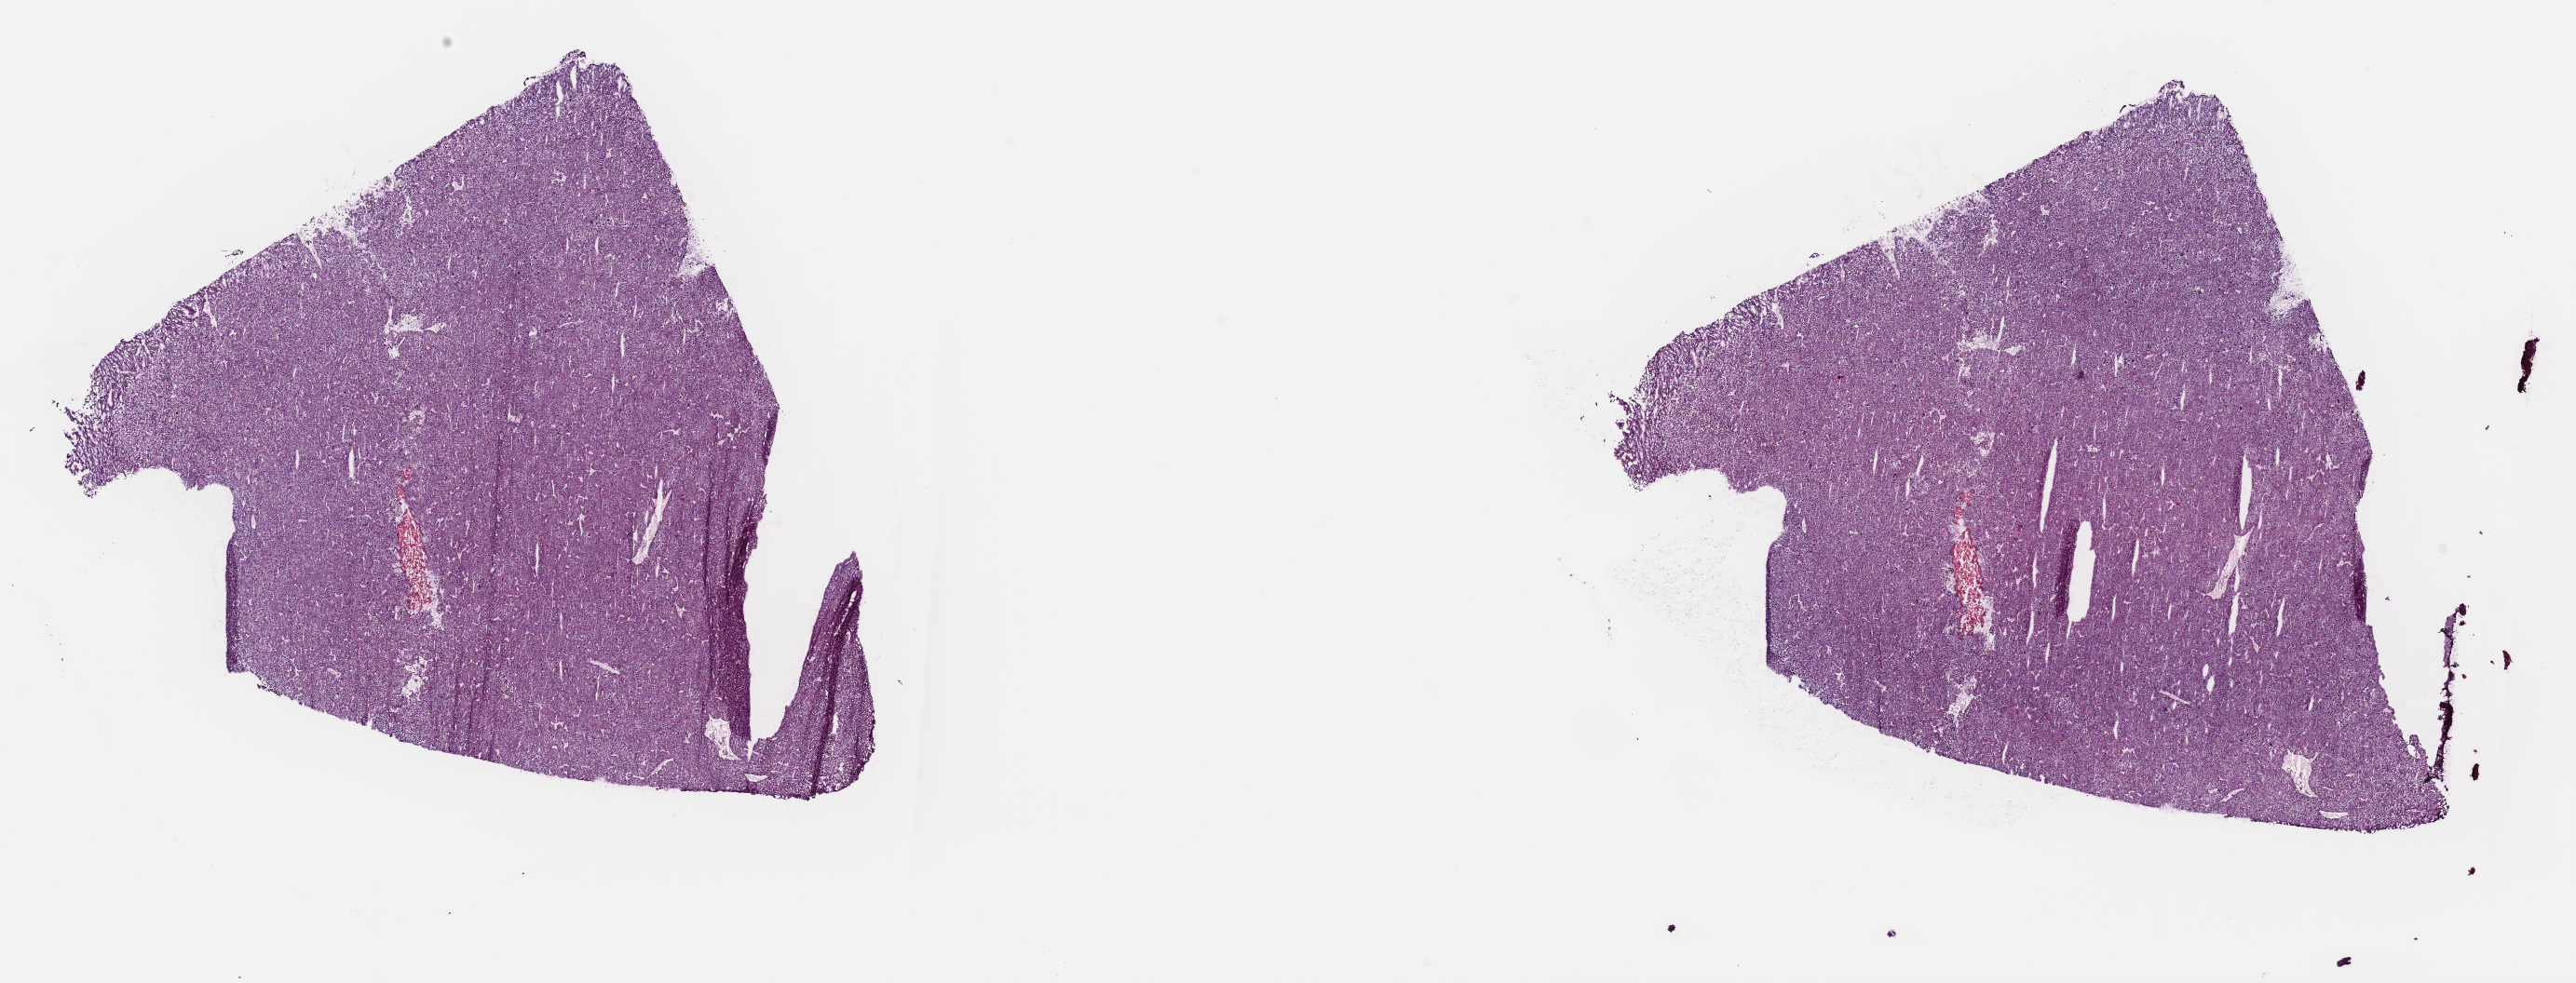
Digitized Hematoxylin and eosin (H&E) stained tissue section (whole slide), whole scanned area (about 21.9 x 8.3 mm, slide scanned at 40x) shown as a low-resolution overview, frozen section from the top of the tissue portion, primary tumour sample from the liver. Female, age 72 years at initial diagnosis. Histologic grade: G2 (moderately differentiated). Slide review estimates, as recorded: tumour cells 96%, tumour nuclei 96%, normal cells 0%, stromal cells 2%, necrosis 2%. Infiltration values recorded for this section: lymphocyte infiltration 1%, monocyte infiltration 1%, neutrophil infiltration 0%.
Histologic diagnosis: Hepatocellular carcinoma, NOS. AJCC pathologic stage: I (7th edition).